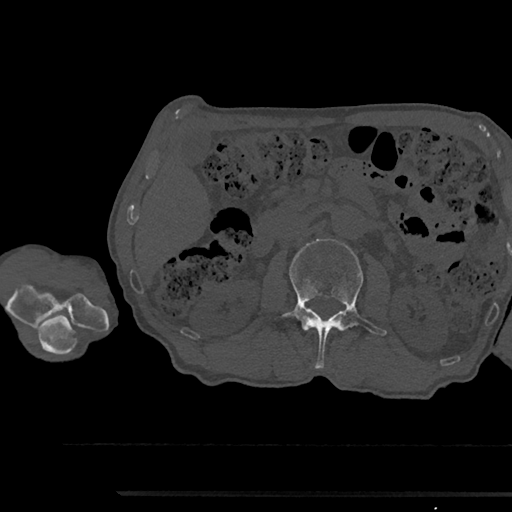
CT including the spine, one axial slice. Position 566 of 797 along the scan axis. Reconstruction kernel Br40s/3. Bone window (W 1800 / L 400 HU). 0.5 mm slice thickness. 512 × 512 image matrix. Male patient, age 79 years. From the clinical record (not read from this slice): primary cancer: prostate.
Annotated regions visible in this slice (semi-automatic segmentation, software-assisted and operator-edited):
- L2 vertebra: bounding box <272,239,386,369> (left, top, right, bottom; pixels)